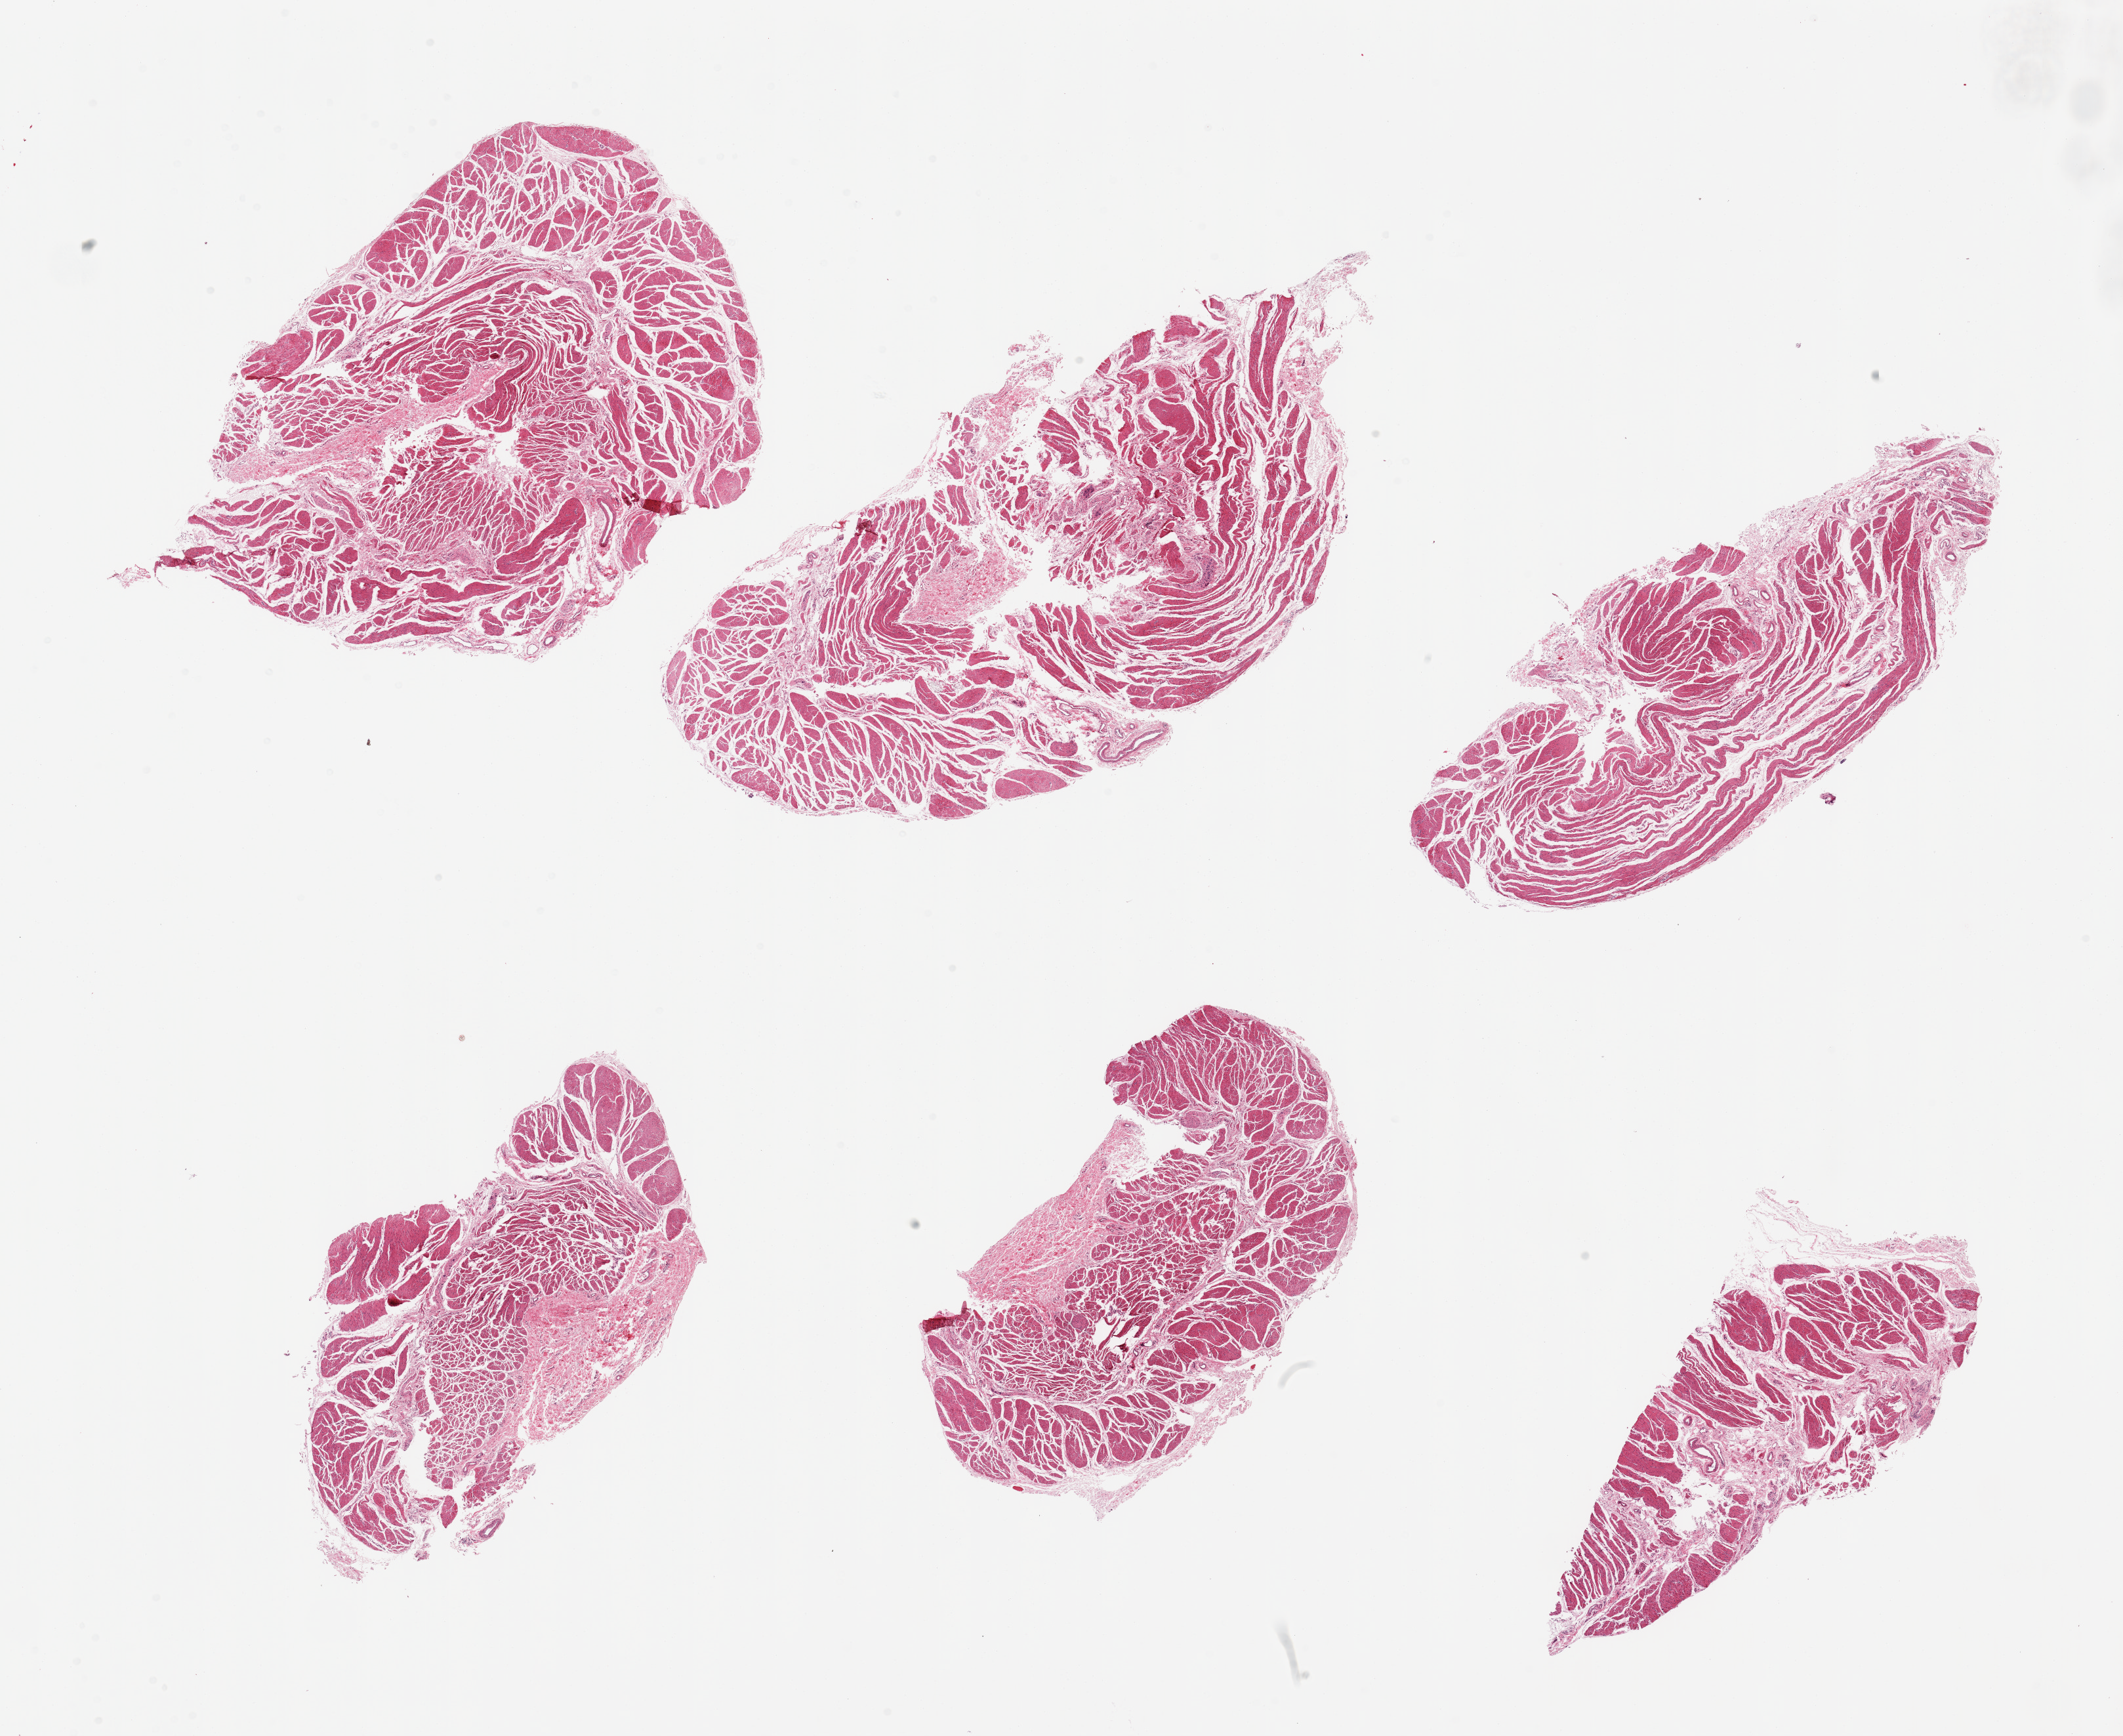
Hematoxylin and eosin (H&E) whole-slide image, whole scanned area (about 25.6 x 20.9 mm) shown as a low-resolution overview, PAXgene-fixed paraffin-embedded (PFPE) section, section of esophageal muscle (target tissue), donor tissue sample.
- review note (as recorded): 6 pieces; well trimmed